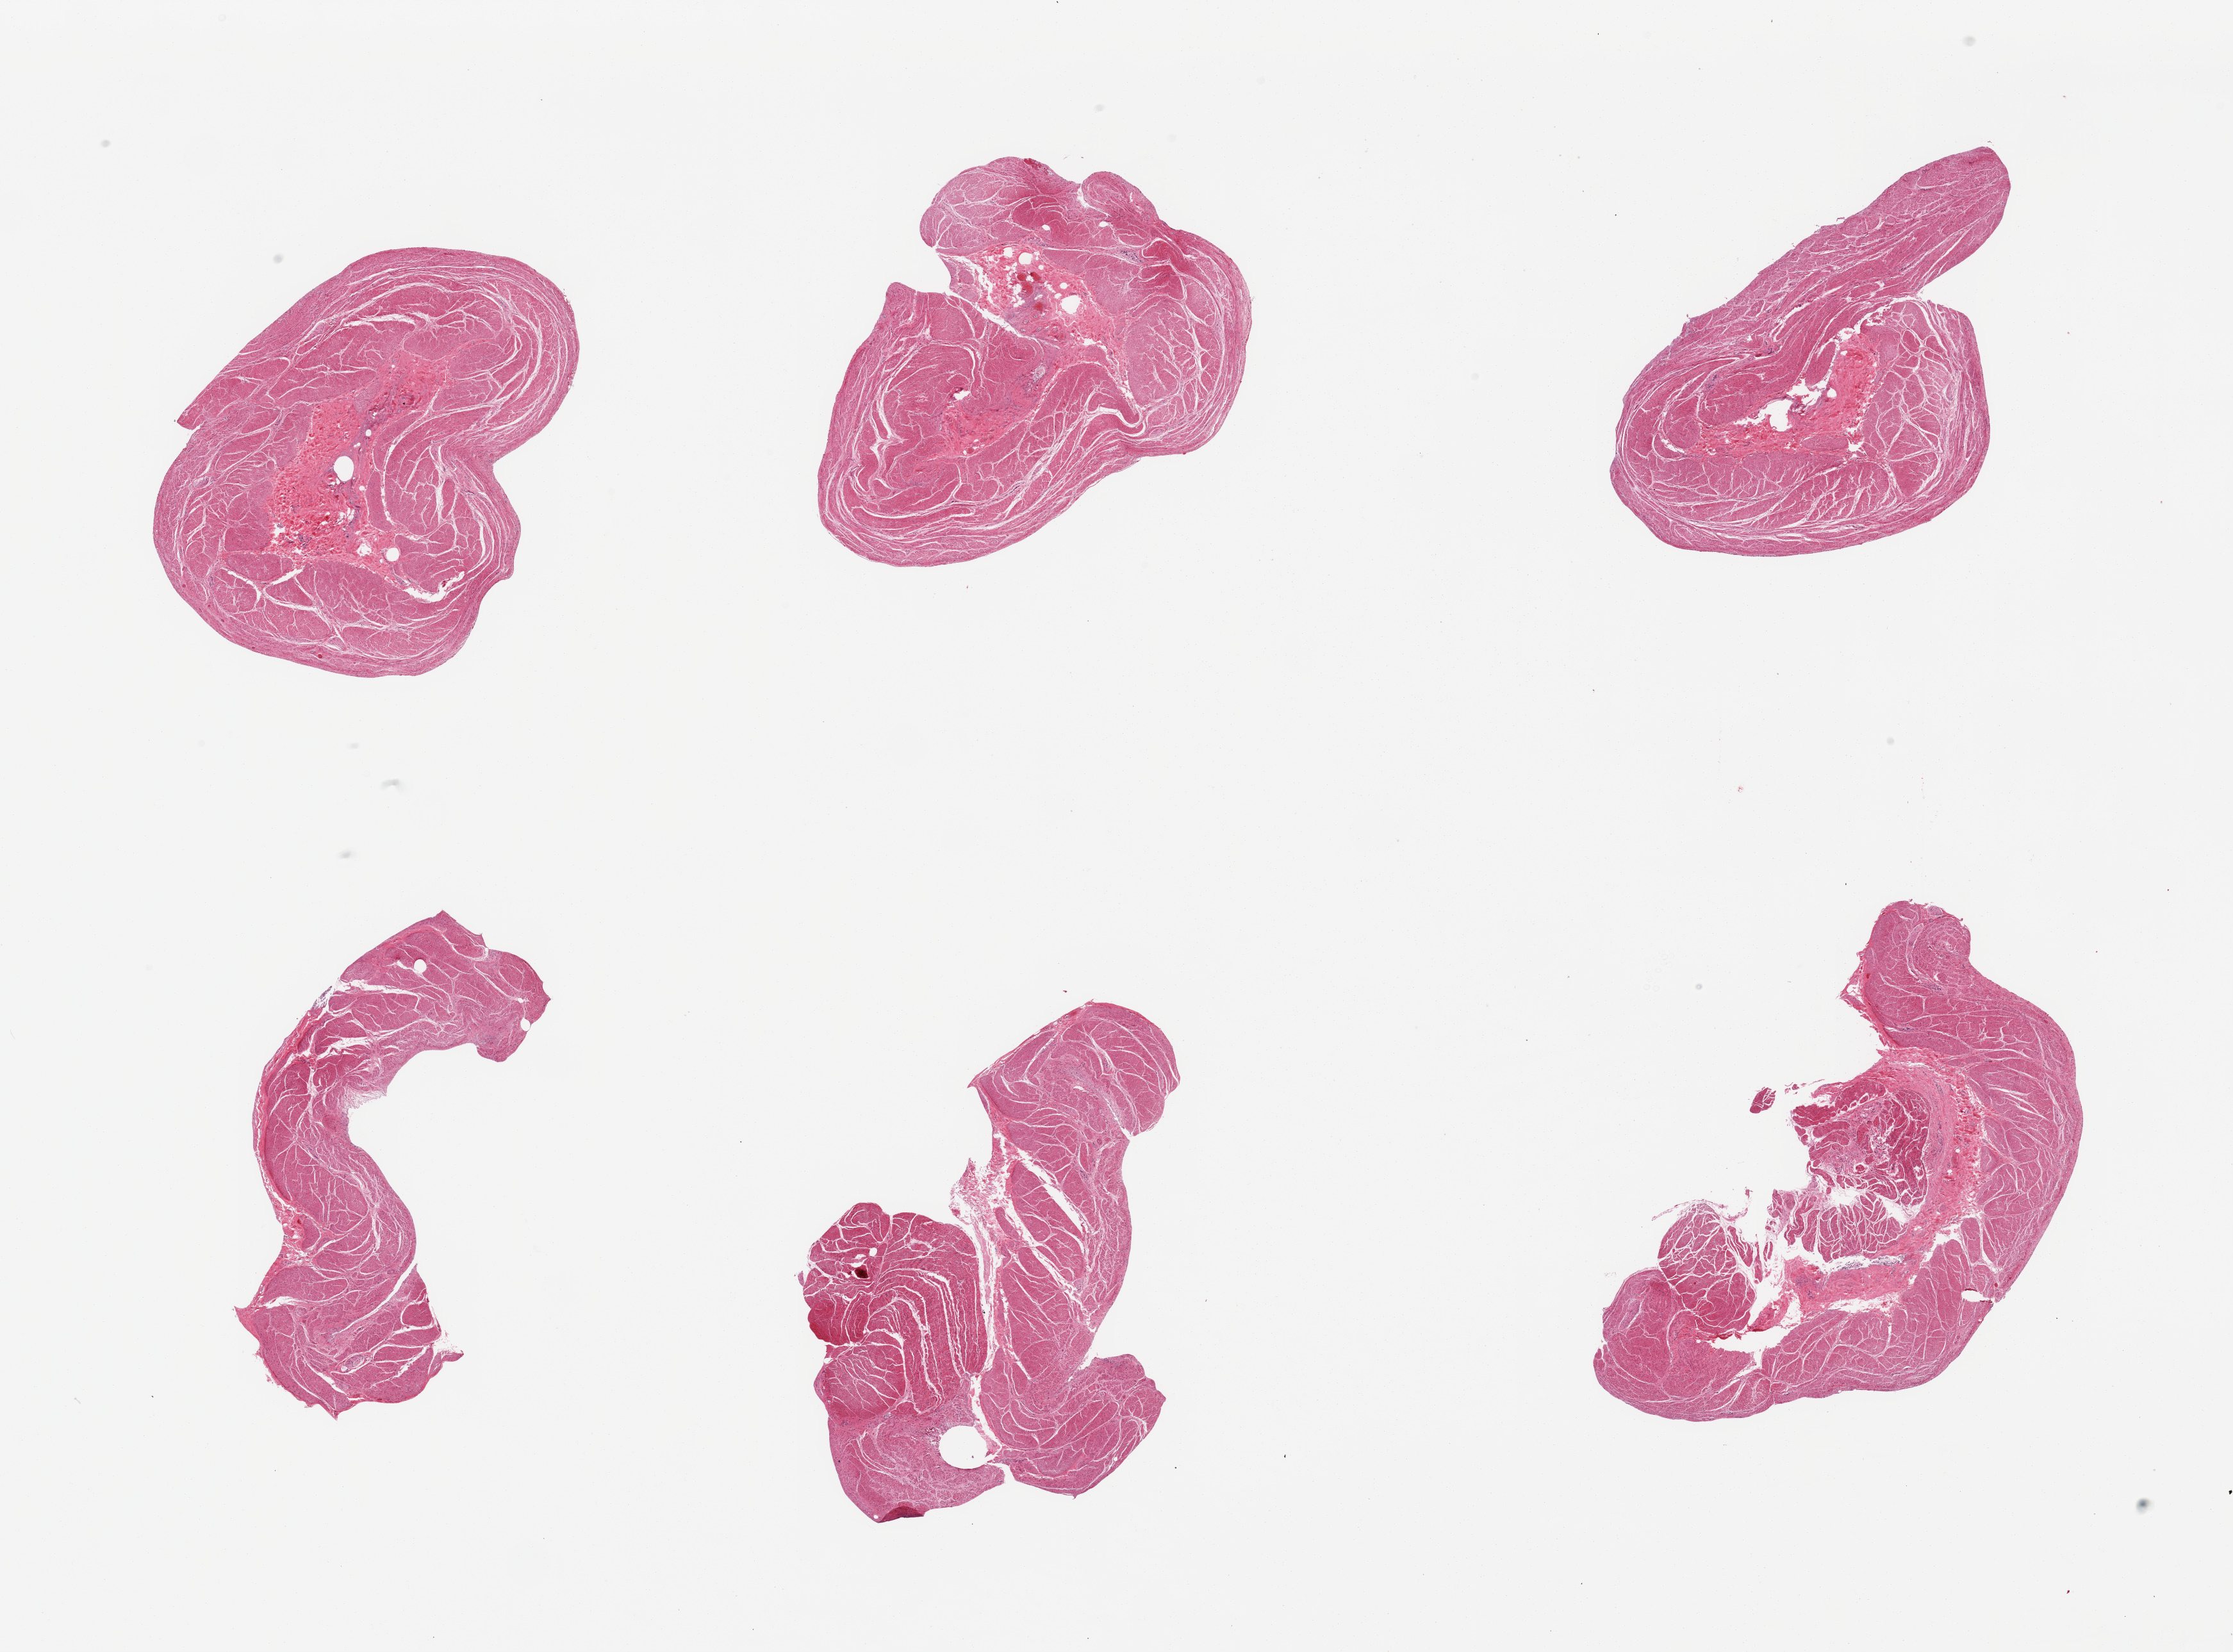
H&E whole-slide image — shown as a low-resolution overview of the whole scanned area (about 27.6 x 20.4 mm), PAXgene-fixed paraffin-embedded (PFPE) section, section of stomach (target tissue), donor tissue sample.
Pathologist's review note for this sample: 6 pieces, mucosa completely sloughed.